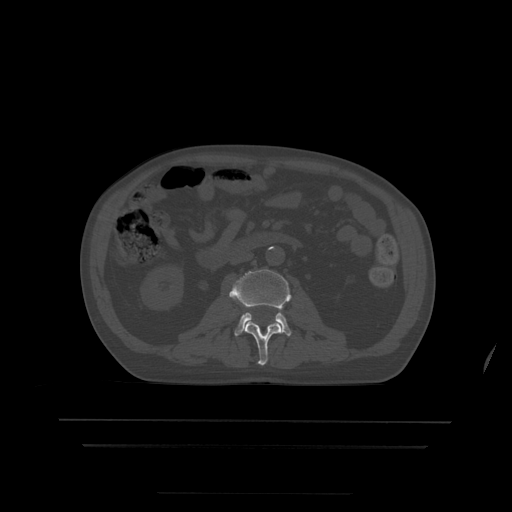
CT including the spine, one axial slice; slice 132 of 522 in the series (ordered by position); bone window (W 1800 / L 400 HU); 1.25 mm slice thickness; 512 × 512 image matrix, field of view 436 × 436 mm. Patient age 68 years. Case-level facts recorded for this patient, not image findings: primary cancer: urothelial.
Annotated regions visible in this slice (semi-automatic segmentation, software-assisted and operator-edited):
- L2 vertebra: bounding box [x1, y1, x2, y2] px = [245, 321, 282, 366]
- L3 vertebra: [229, 270, 292, 336]